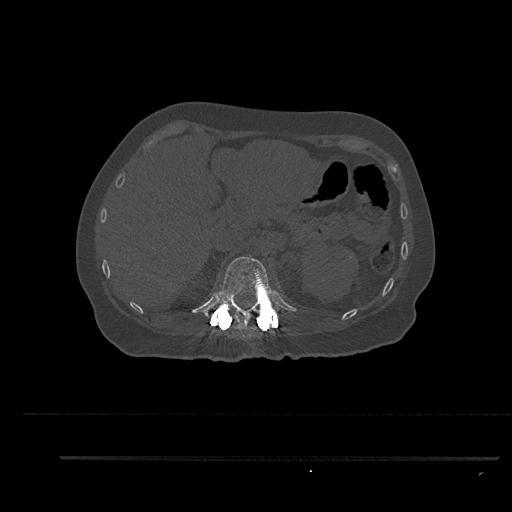
CT including the spine, one axial slice. Position 266 of 797 along the scan axis. Reconstruction kernel Br40s/3. 120 kVp. Bone window (W 1800 / L 400 HU). 512 × 512 image matrix, field of view 408 × 408 mm. Patient: female, 44 years. From the clinical record (not read from this slice): primary cancer: renal; vertebrae with lytic lesions (as recorded): L1.
Outlined on this slice (semi-automatically segmented with operator editing):
- T12 vertebra: box from (x=208, y=255) to (x=281, y=329) px